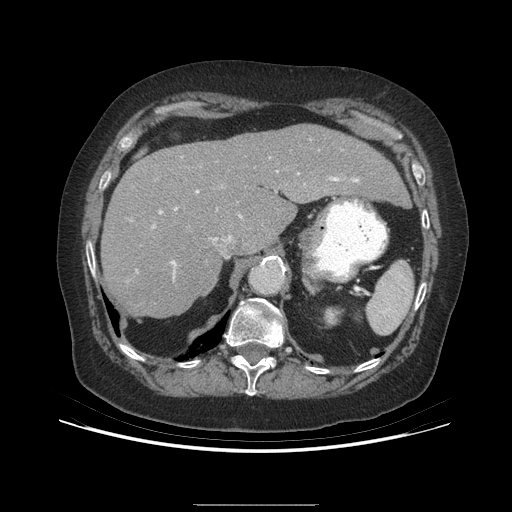
Contrast-enhanced abdominal CT (liver protocol), one axial slice. Slice 165 of 192 in the series (ordered by position). Reconstruction kernel STANDARD. 140 kVp. Soft-tissue window (W 400 / L 40 HU). 512 × 512 image matrix. From the clinical record (not read from this slice): diagnosis: hepatocellular carcinoma (patient treated with transarterial chemoembolisation; whether this scan precedes or follows treatment is not stated here); TNM stage (as recorded): Stage-I; Child-Pugh class: A; tumour differentiation: moderately differentiated; tumour size: 3.2 cm.
Structures marked on this image (semi-automatically segmented with operator editing):
- liver parenchyma outside the tumour (the mass and vessels are separate outlines, so this box may not span the whole liver): bounding box [x1, y1, x2, y2] px = [100, 124, 406, 316]
- liver vessels: [153, 173, 358, 273]